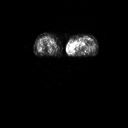
FDG PET of an extremity soft-tissue mass (from a PET/CT study), one axial slice; slice 11 of 91 in the series (ordered by position); 3.27 mm slice thickness; 128 × 128 image matrix, field of view 700 × 700 mm. Female patient, age 74 years. Case-level facts recorded for this patient, not image findings: histological type: pleomorphic leiomyosarcoma; grade: high; site of the primary tumour: left thigh.
Annotated regions visible in this slice (expert contour drawn on MRI and transferred to this co-registered scan by the dataset authors):
- gross tumour volume including surrounding oedema: bounding box <71,38,87,52> (left, top, right, bottom; pixels)